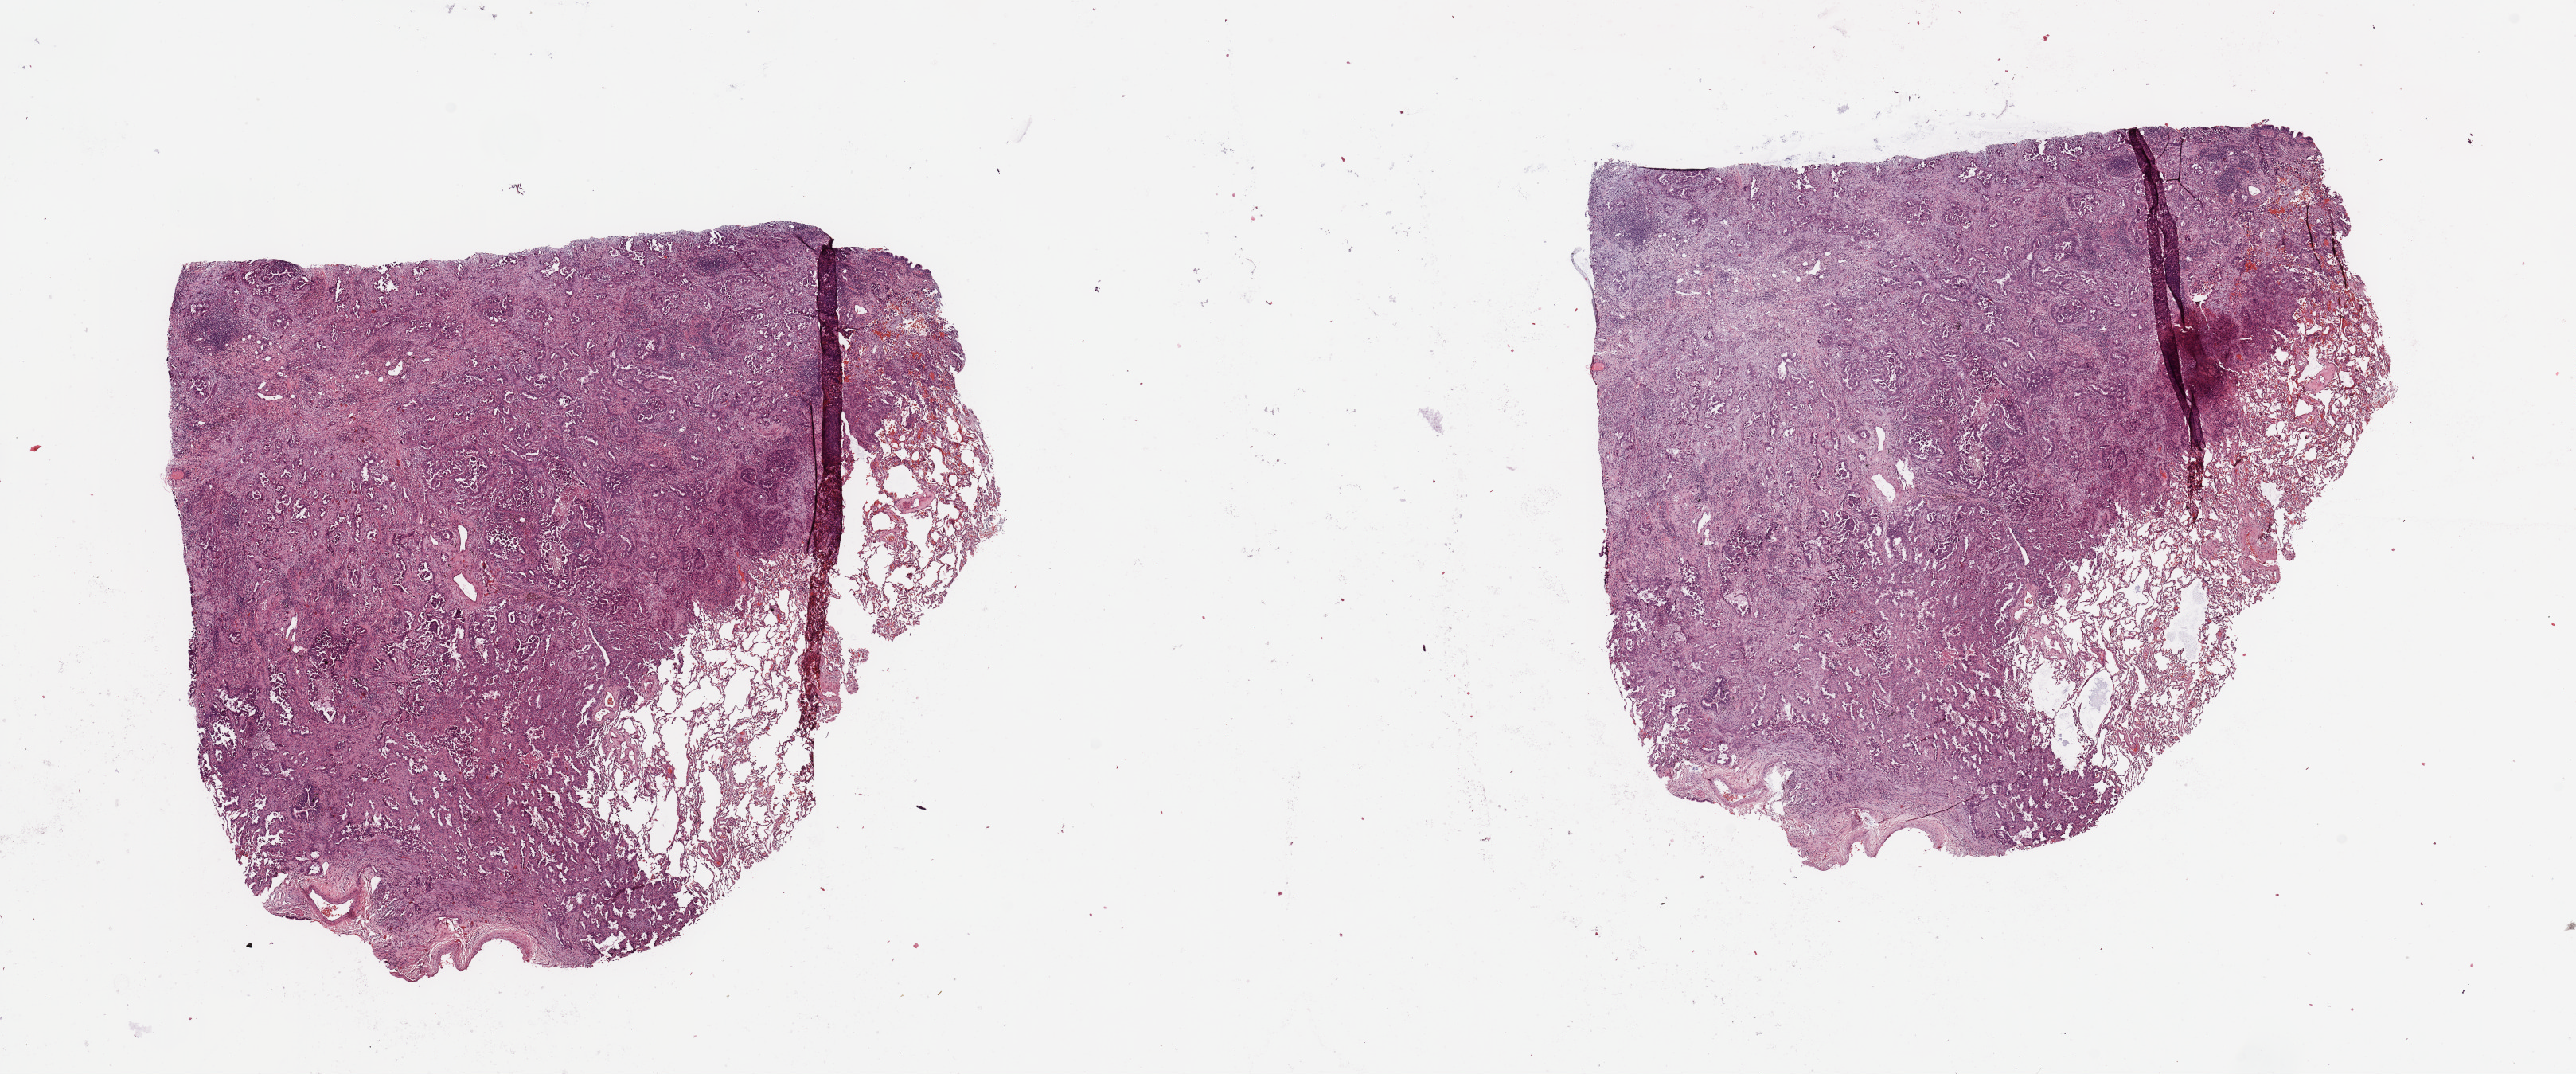
Whole-slide histology image, Hematoxylin and eosin (H&E) stained, a low-resolution overview of the entire scanned area, about 25.6 x 10.7 mm, tumour tissue sample, lung. 67-year-old female patient. Histologic grade: G2 (moderately differentiated).
- AJCC pathologic stage: II
- histologic diagnosis: Adenocarcinoma, NOS